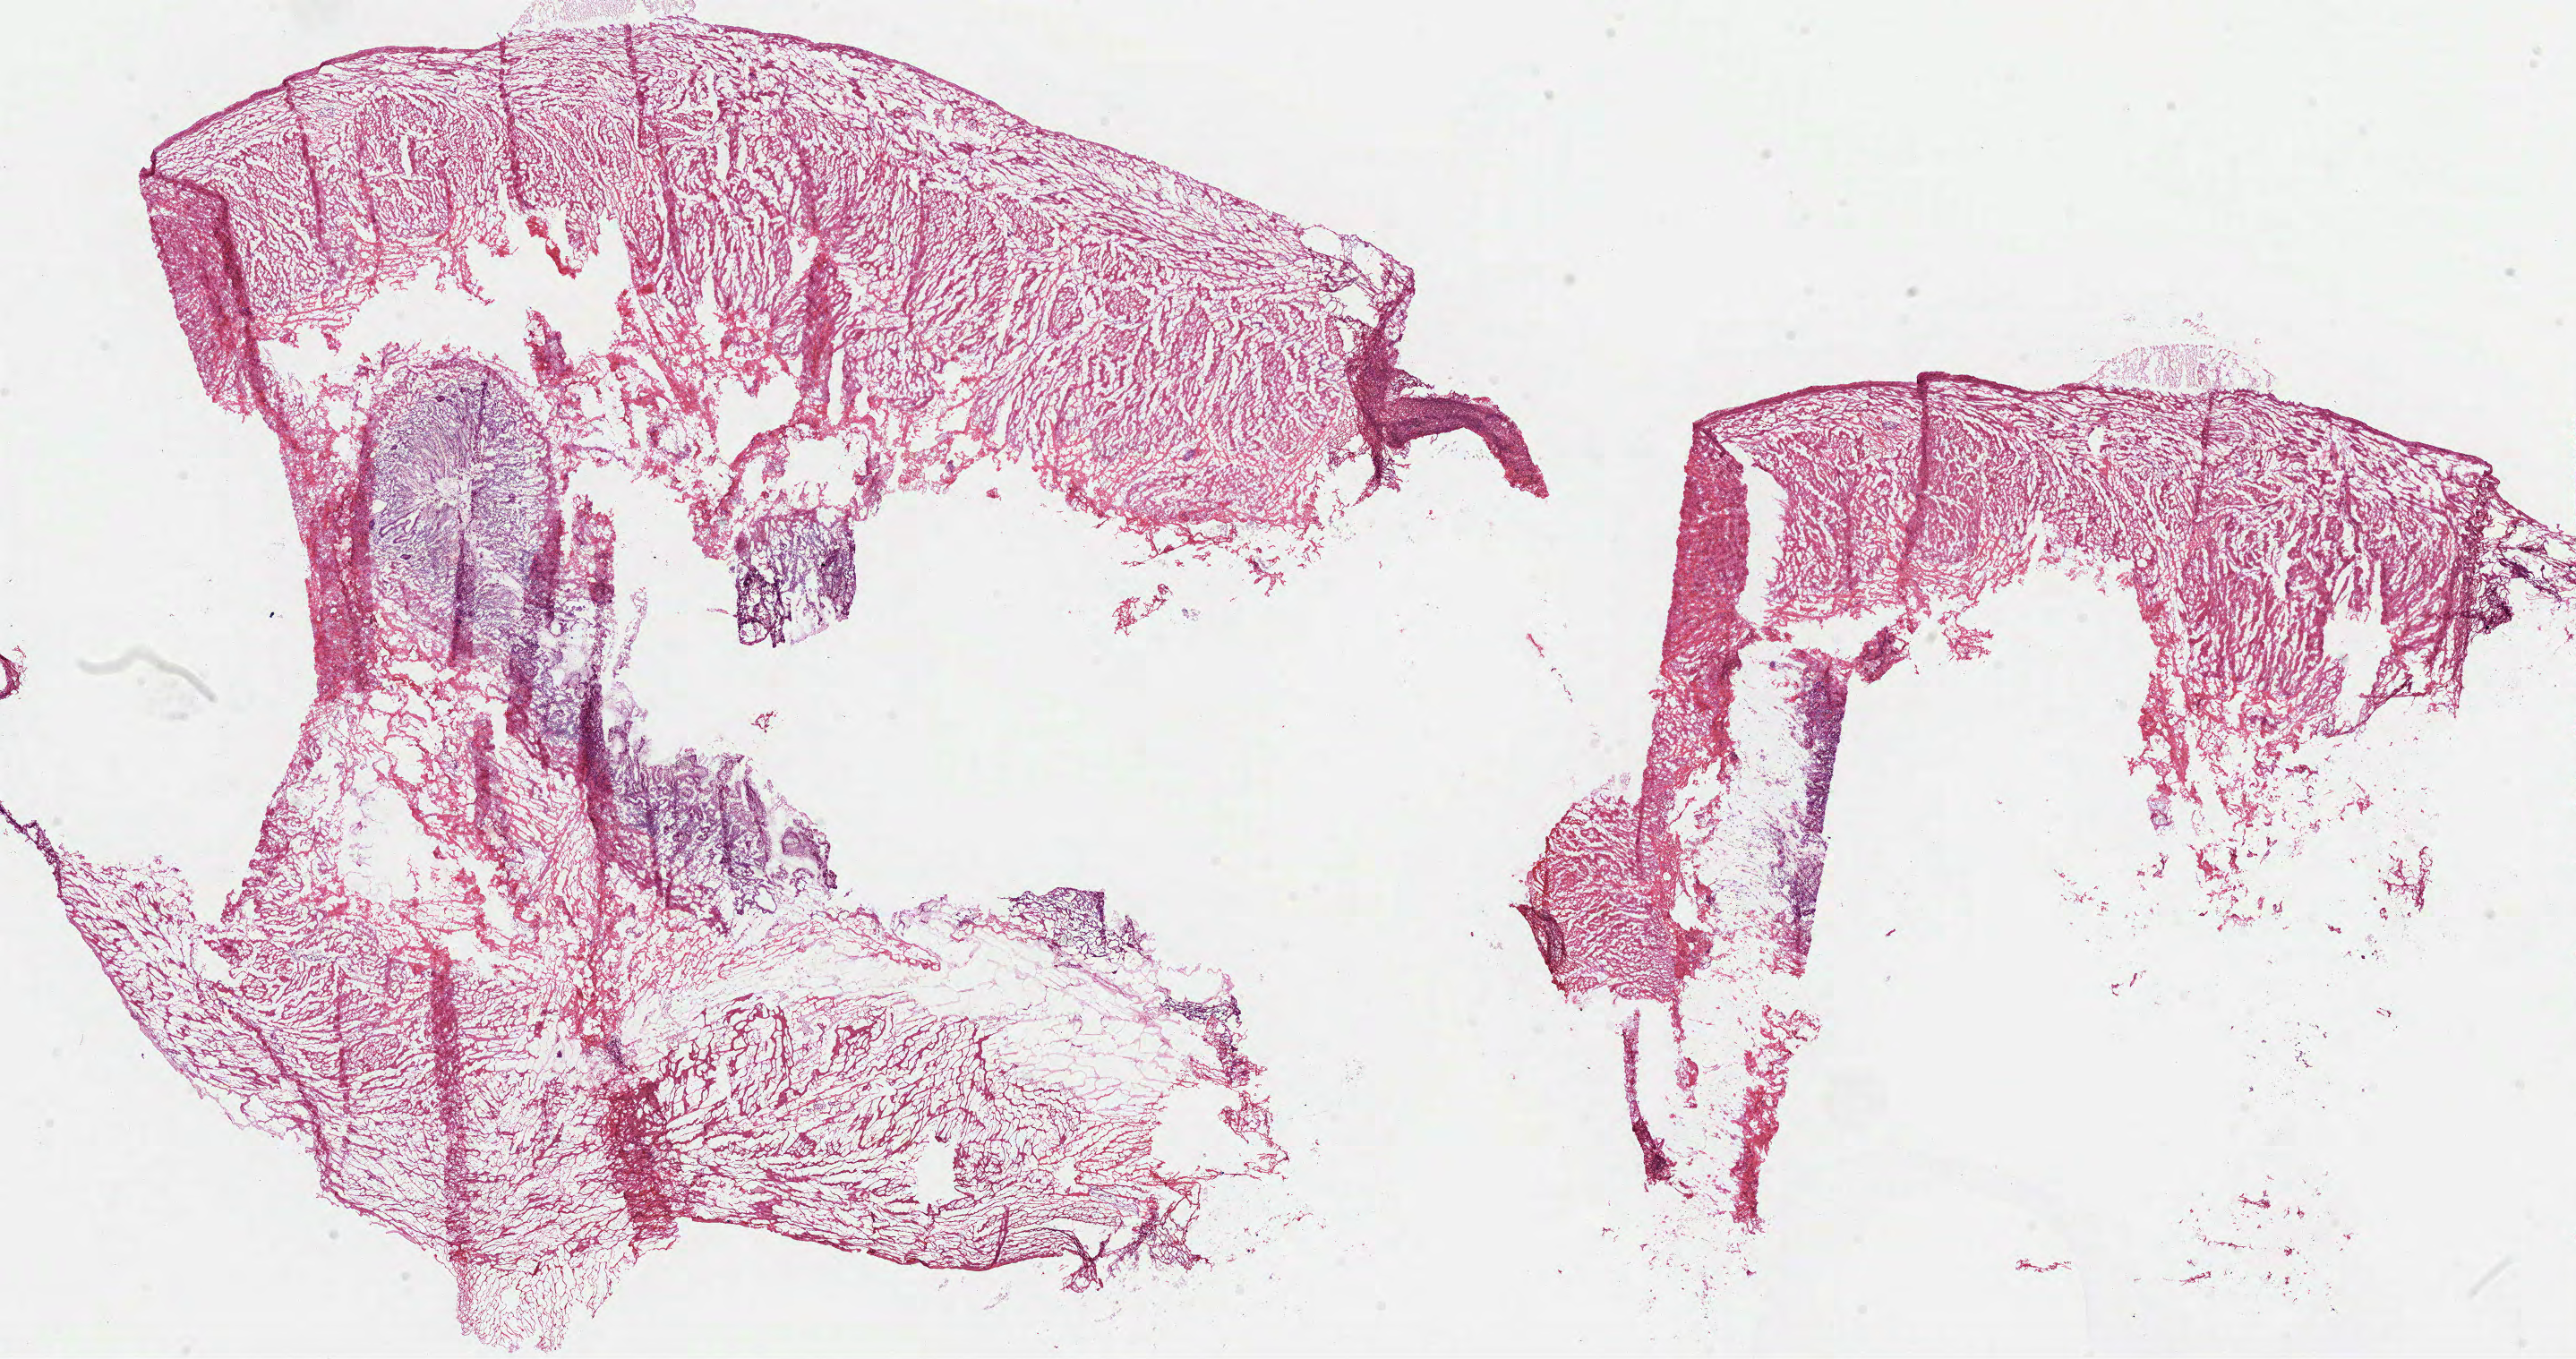
Whole-slide histology image, H&E, low-resolution overview of the scanned area, about 23.2 x 12.2 mm; frozen section from the top of the tissue portion; sample: solid tissue normal (non-tumour tissue), stomach. Female, age 69 years at initial diagnosis.
This section: solid tissue normal (non-tumour) sample from the same patient. Patient diagnosis: Adenocarcinoma, intestinal type (body of stomach).